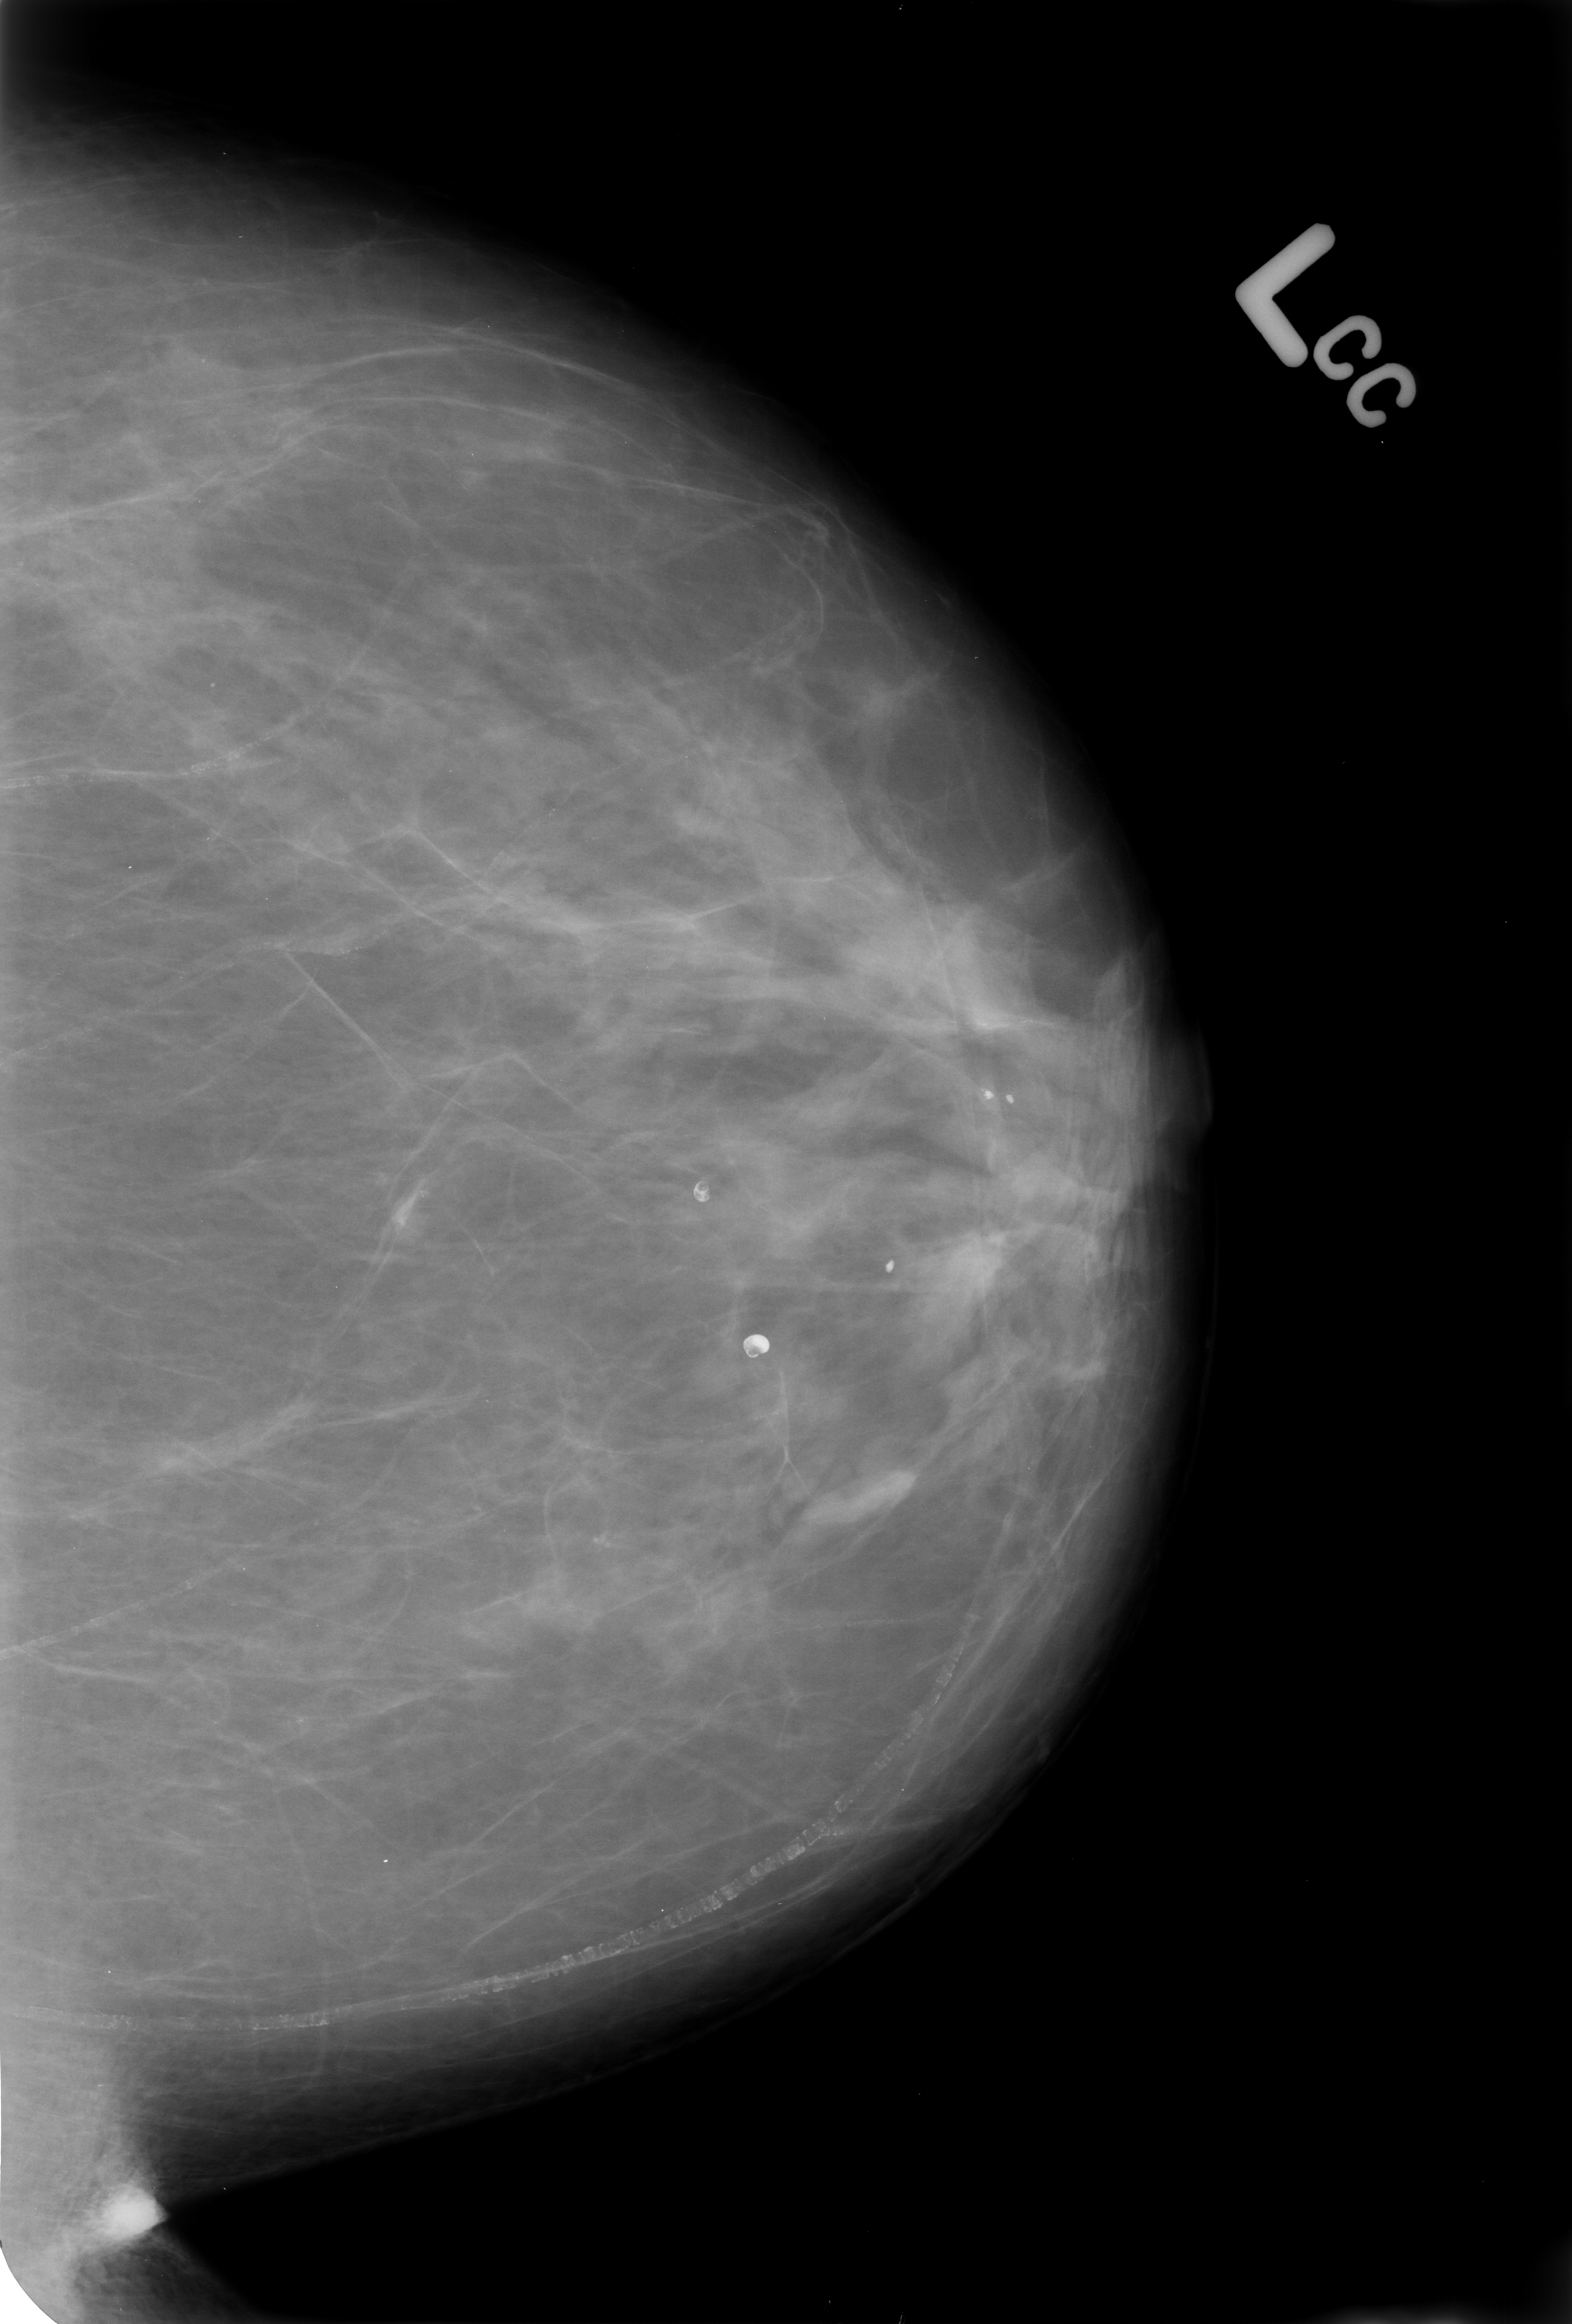
Scanned film-screen mammogram; left breast; CC view; BI-RADS breast density category 2 (scale 1–4).
Radiologist-marked abnormalities on this image: Finding 1 of 4: calcifications, morphology vascular / coarse / lucent centered; BI-RADS assessment category 2; subtlety rating 5 on a 1 (subtle) to 5 (obvious) scale; benign without callback (not worked up further). Finding 2 of 4: calcifications, morphology vascular / coarse / lucent centered; BI-RADS assessment category 2; benign without callback (not worked up further). Finding 3 of 4: calcifications, morphology vascular / coarse / lucent centered; BI-RADS assessment category 2; benign; no additional work-up was recommended (benign without callback). Finding 4 of 4: calcifications, morphology vascular / coarse / lucent centered; BI-RADS assessment category 2; benign; no additional work-up was recommended (benign without callback).